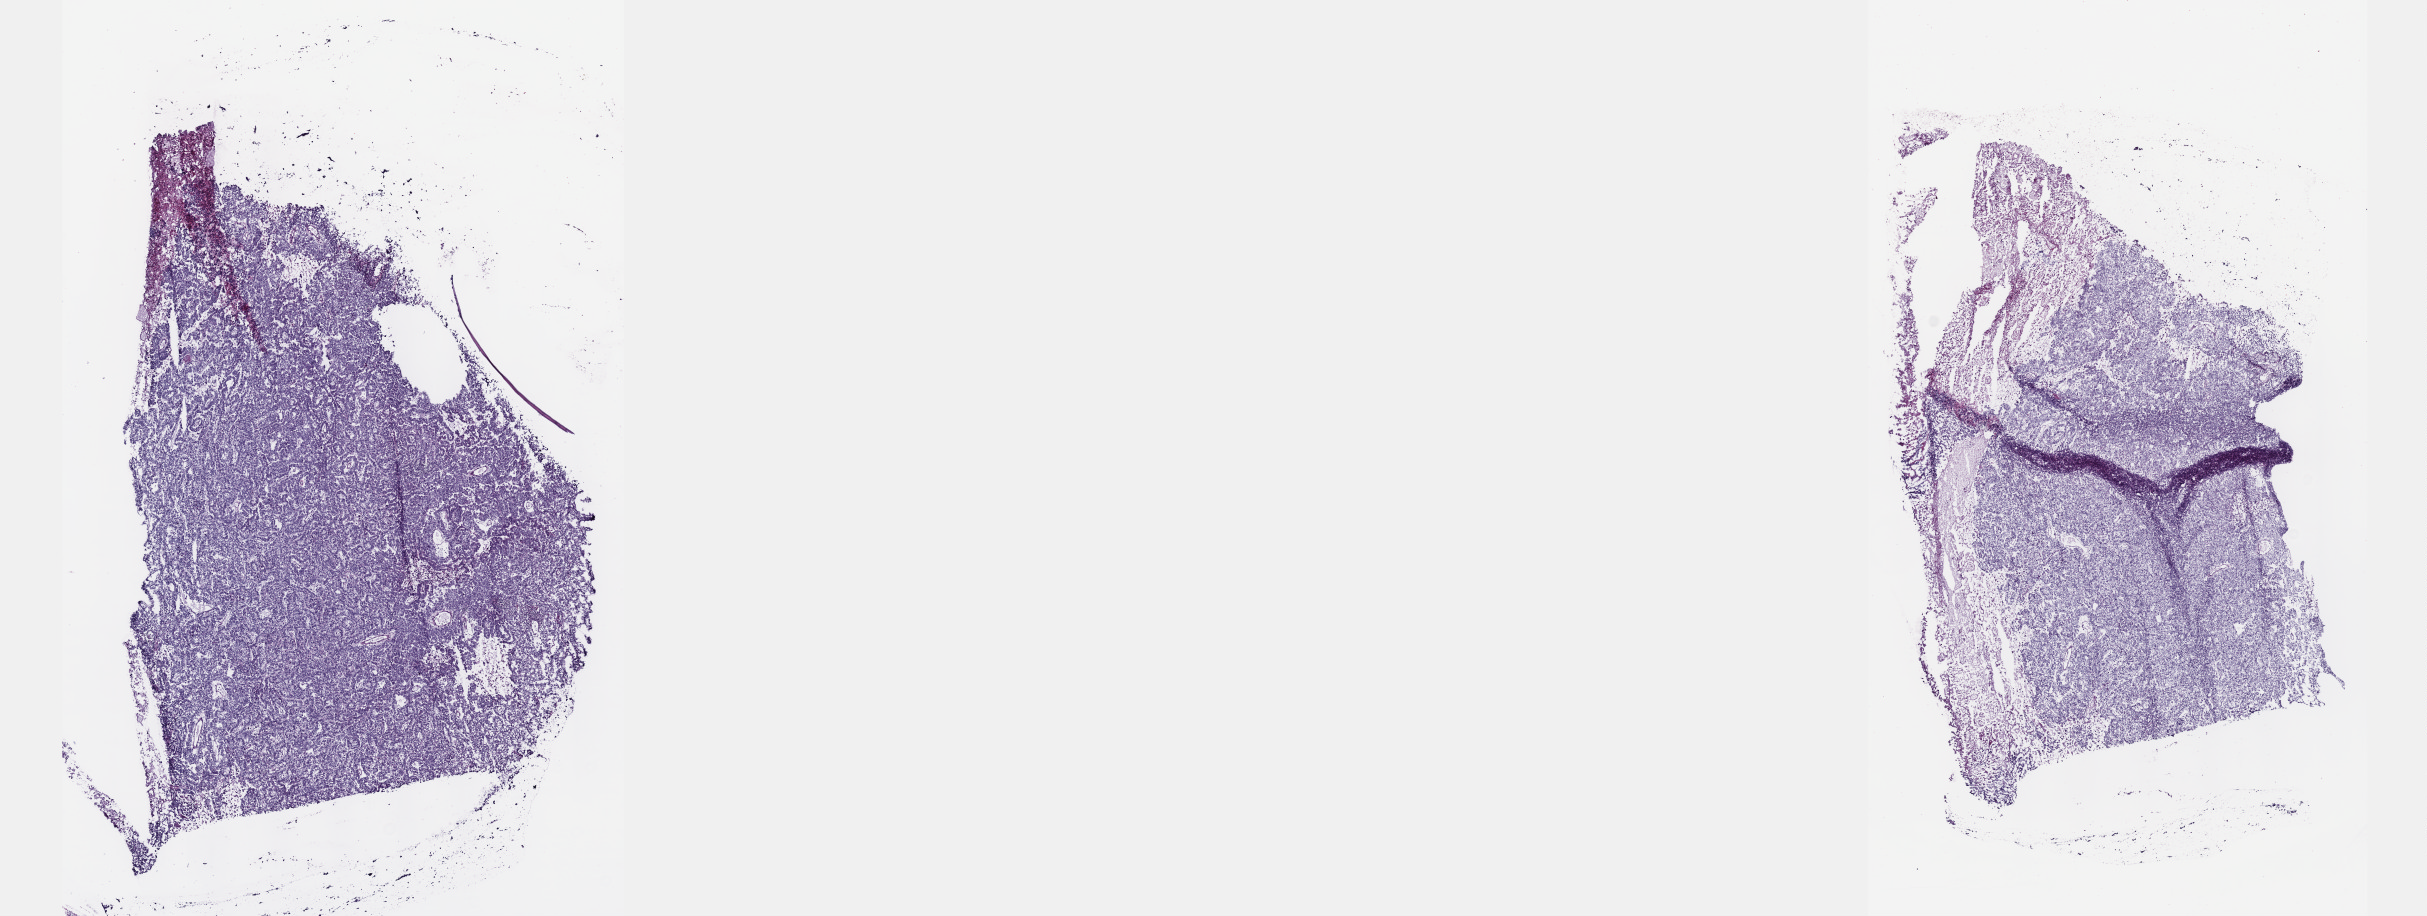
Digitized H&E-stained tissue section (whole slide) — a low-resolution overview of the entire scanned area, about 19.6 x 7.4 mm (slide scanned at 40x); frozen section from the top of the tissue portion; primary tumour sample from the testis. Male, age 38 years at initial diagnosis. Composition of this section per pathologist review: tumour cells 100%, tumour nuclei 80%, normal cells 0%, stromal cells 0%, necrosis 0%. Infiltration values recorded for this section: lymphocyte infiltration 1%, monocyte infiltration 0%, neutrophil infiltration 0%.
• TNM: T1 N0 M0
• AJCC pathologic stage: IS (5th edition)
• laterality: right
• histologic diagnosis: Yolk sac tumor